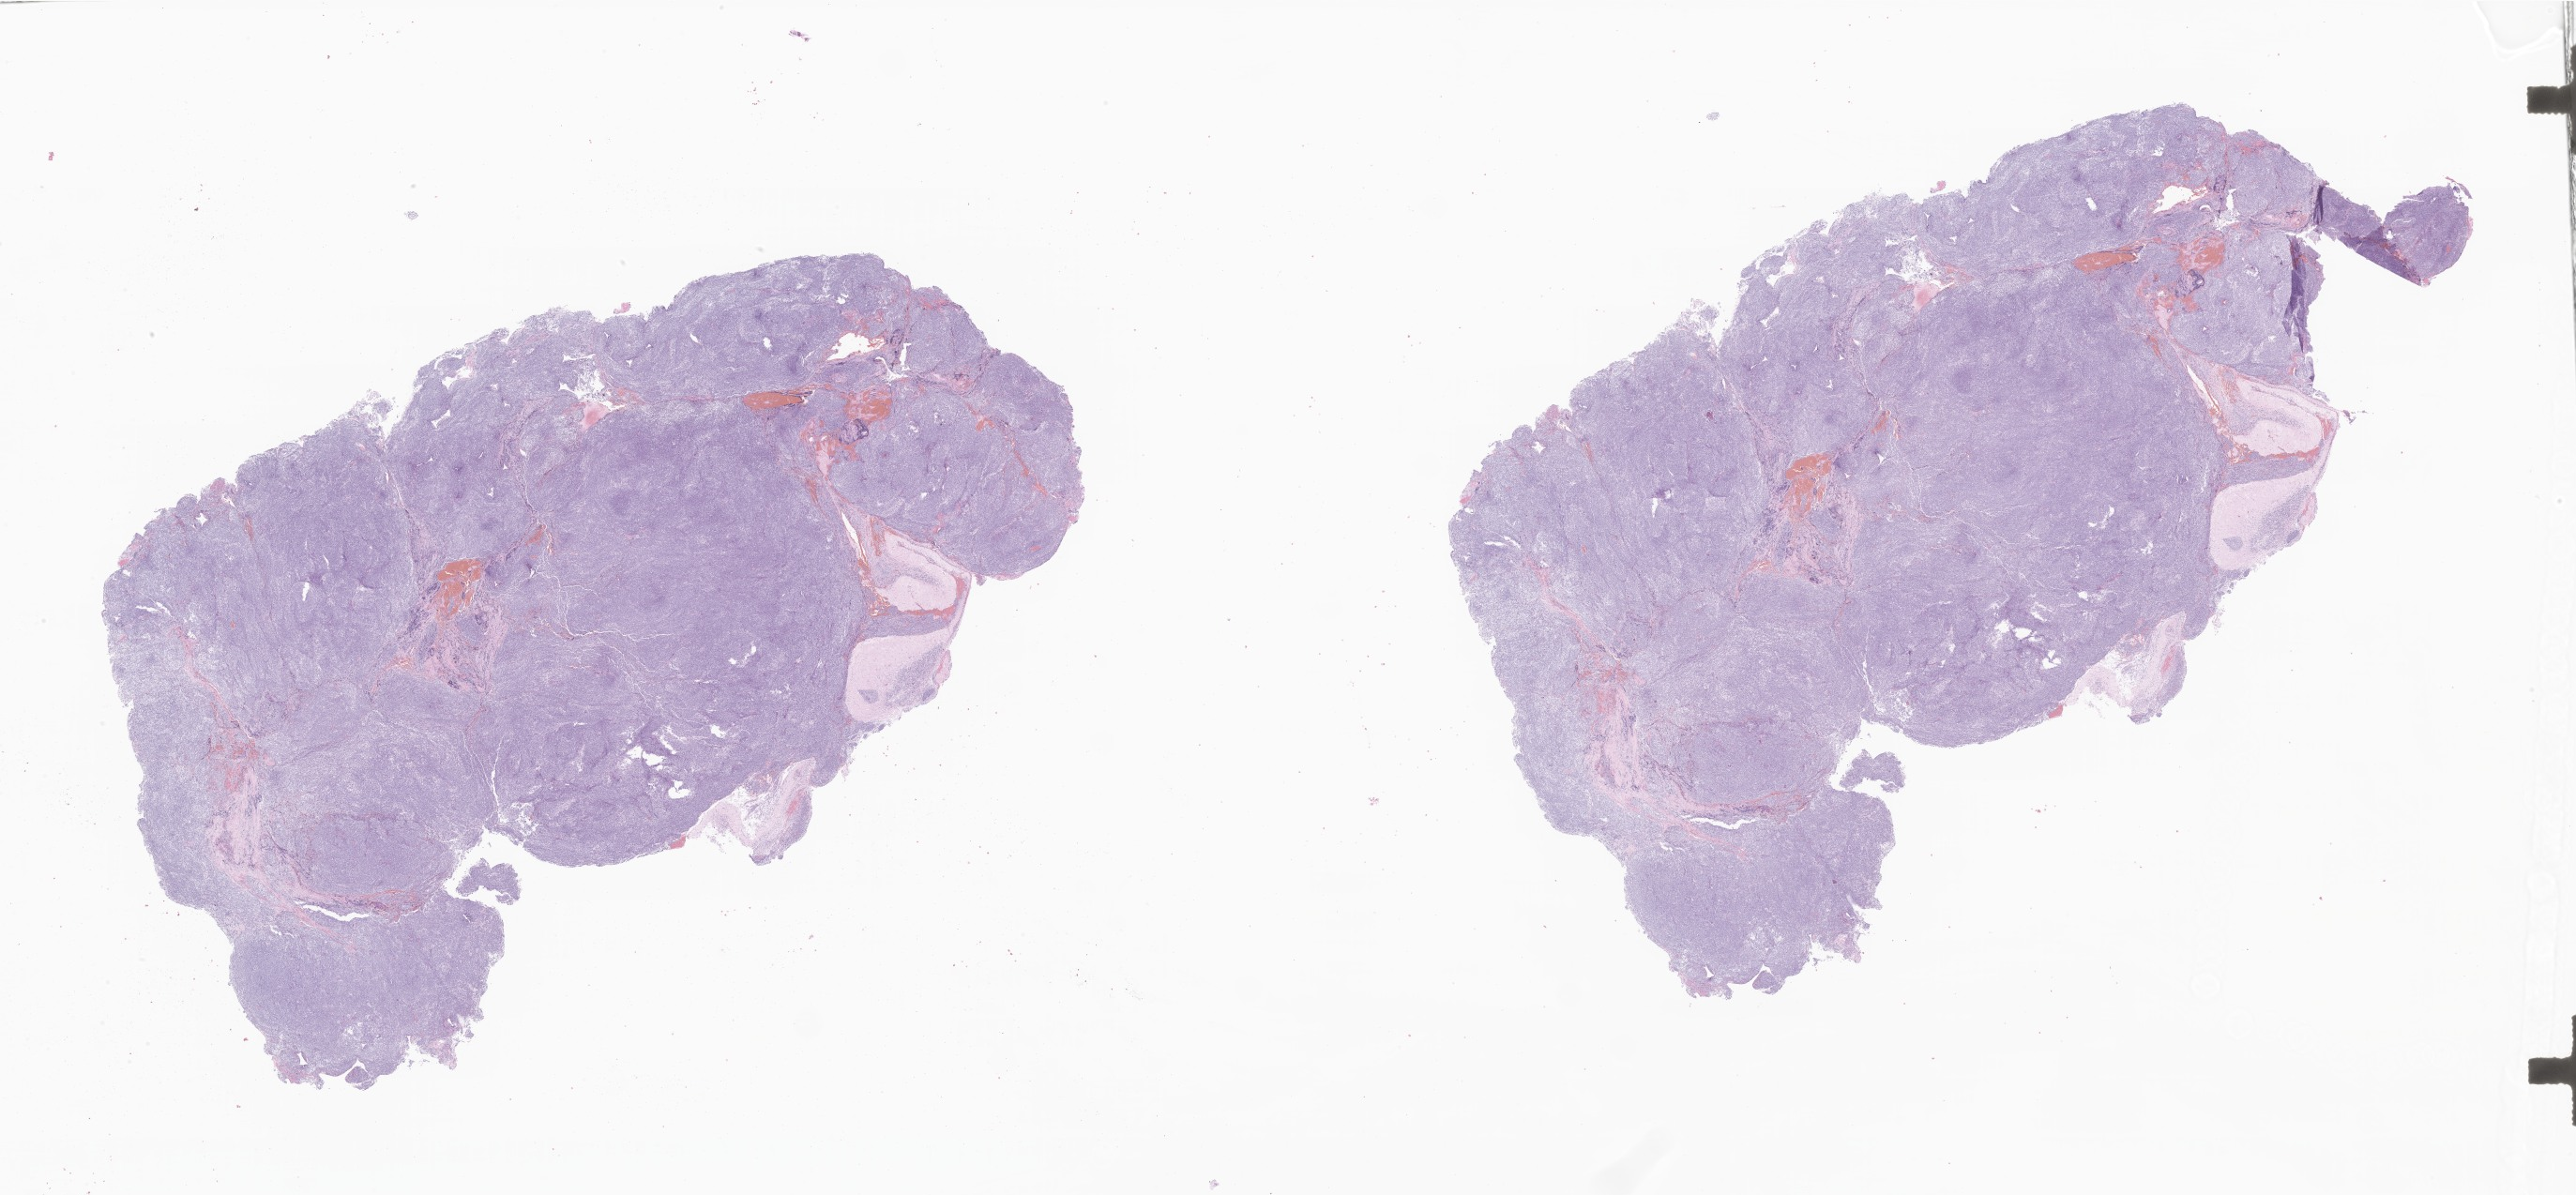
Digitized hematoxylin and eosin (H&E)-stained section of tumor tissue from the brain — a low-resolution overview of the entire scanned area, about 46.3 x 21.5 mm. FFPE section. Female patient, age 198 months (16 years 6 months).
• recorded diagnosis: Neoplasm, malignant